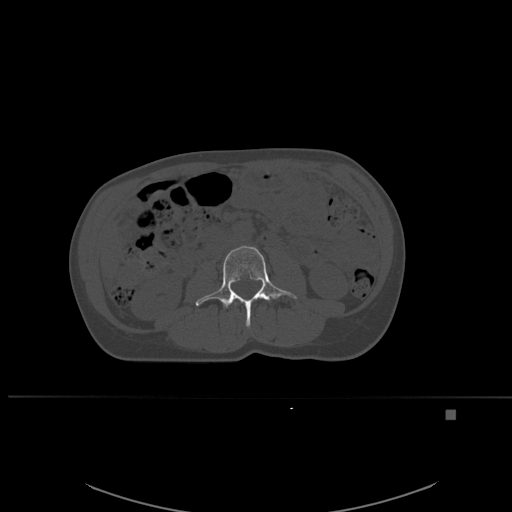
CT including the spine, one axial slice. Slice 216 of 537 in the series (ordered by position). Bone window (W 1800 / L 400 HU). 1.5 mm slice thickness. 512 × 512 image matrix, field of view 440 × 440 mm. Patient: female, 45 years. From the clinical record (not read from this slice): primary cancer: lung.
Annotated regions visible in this slice (semi-automatic segmentation, software-assisted and operator-edited):
- L2 vertebra: bounding box <235,299,255,305> (left, top, right, bottom; pixels)
- L3 vertebra: <196,245,297,328>